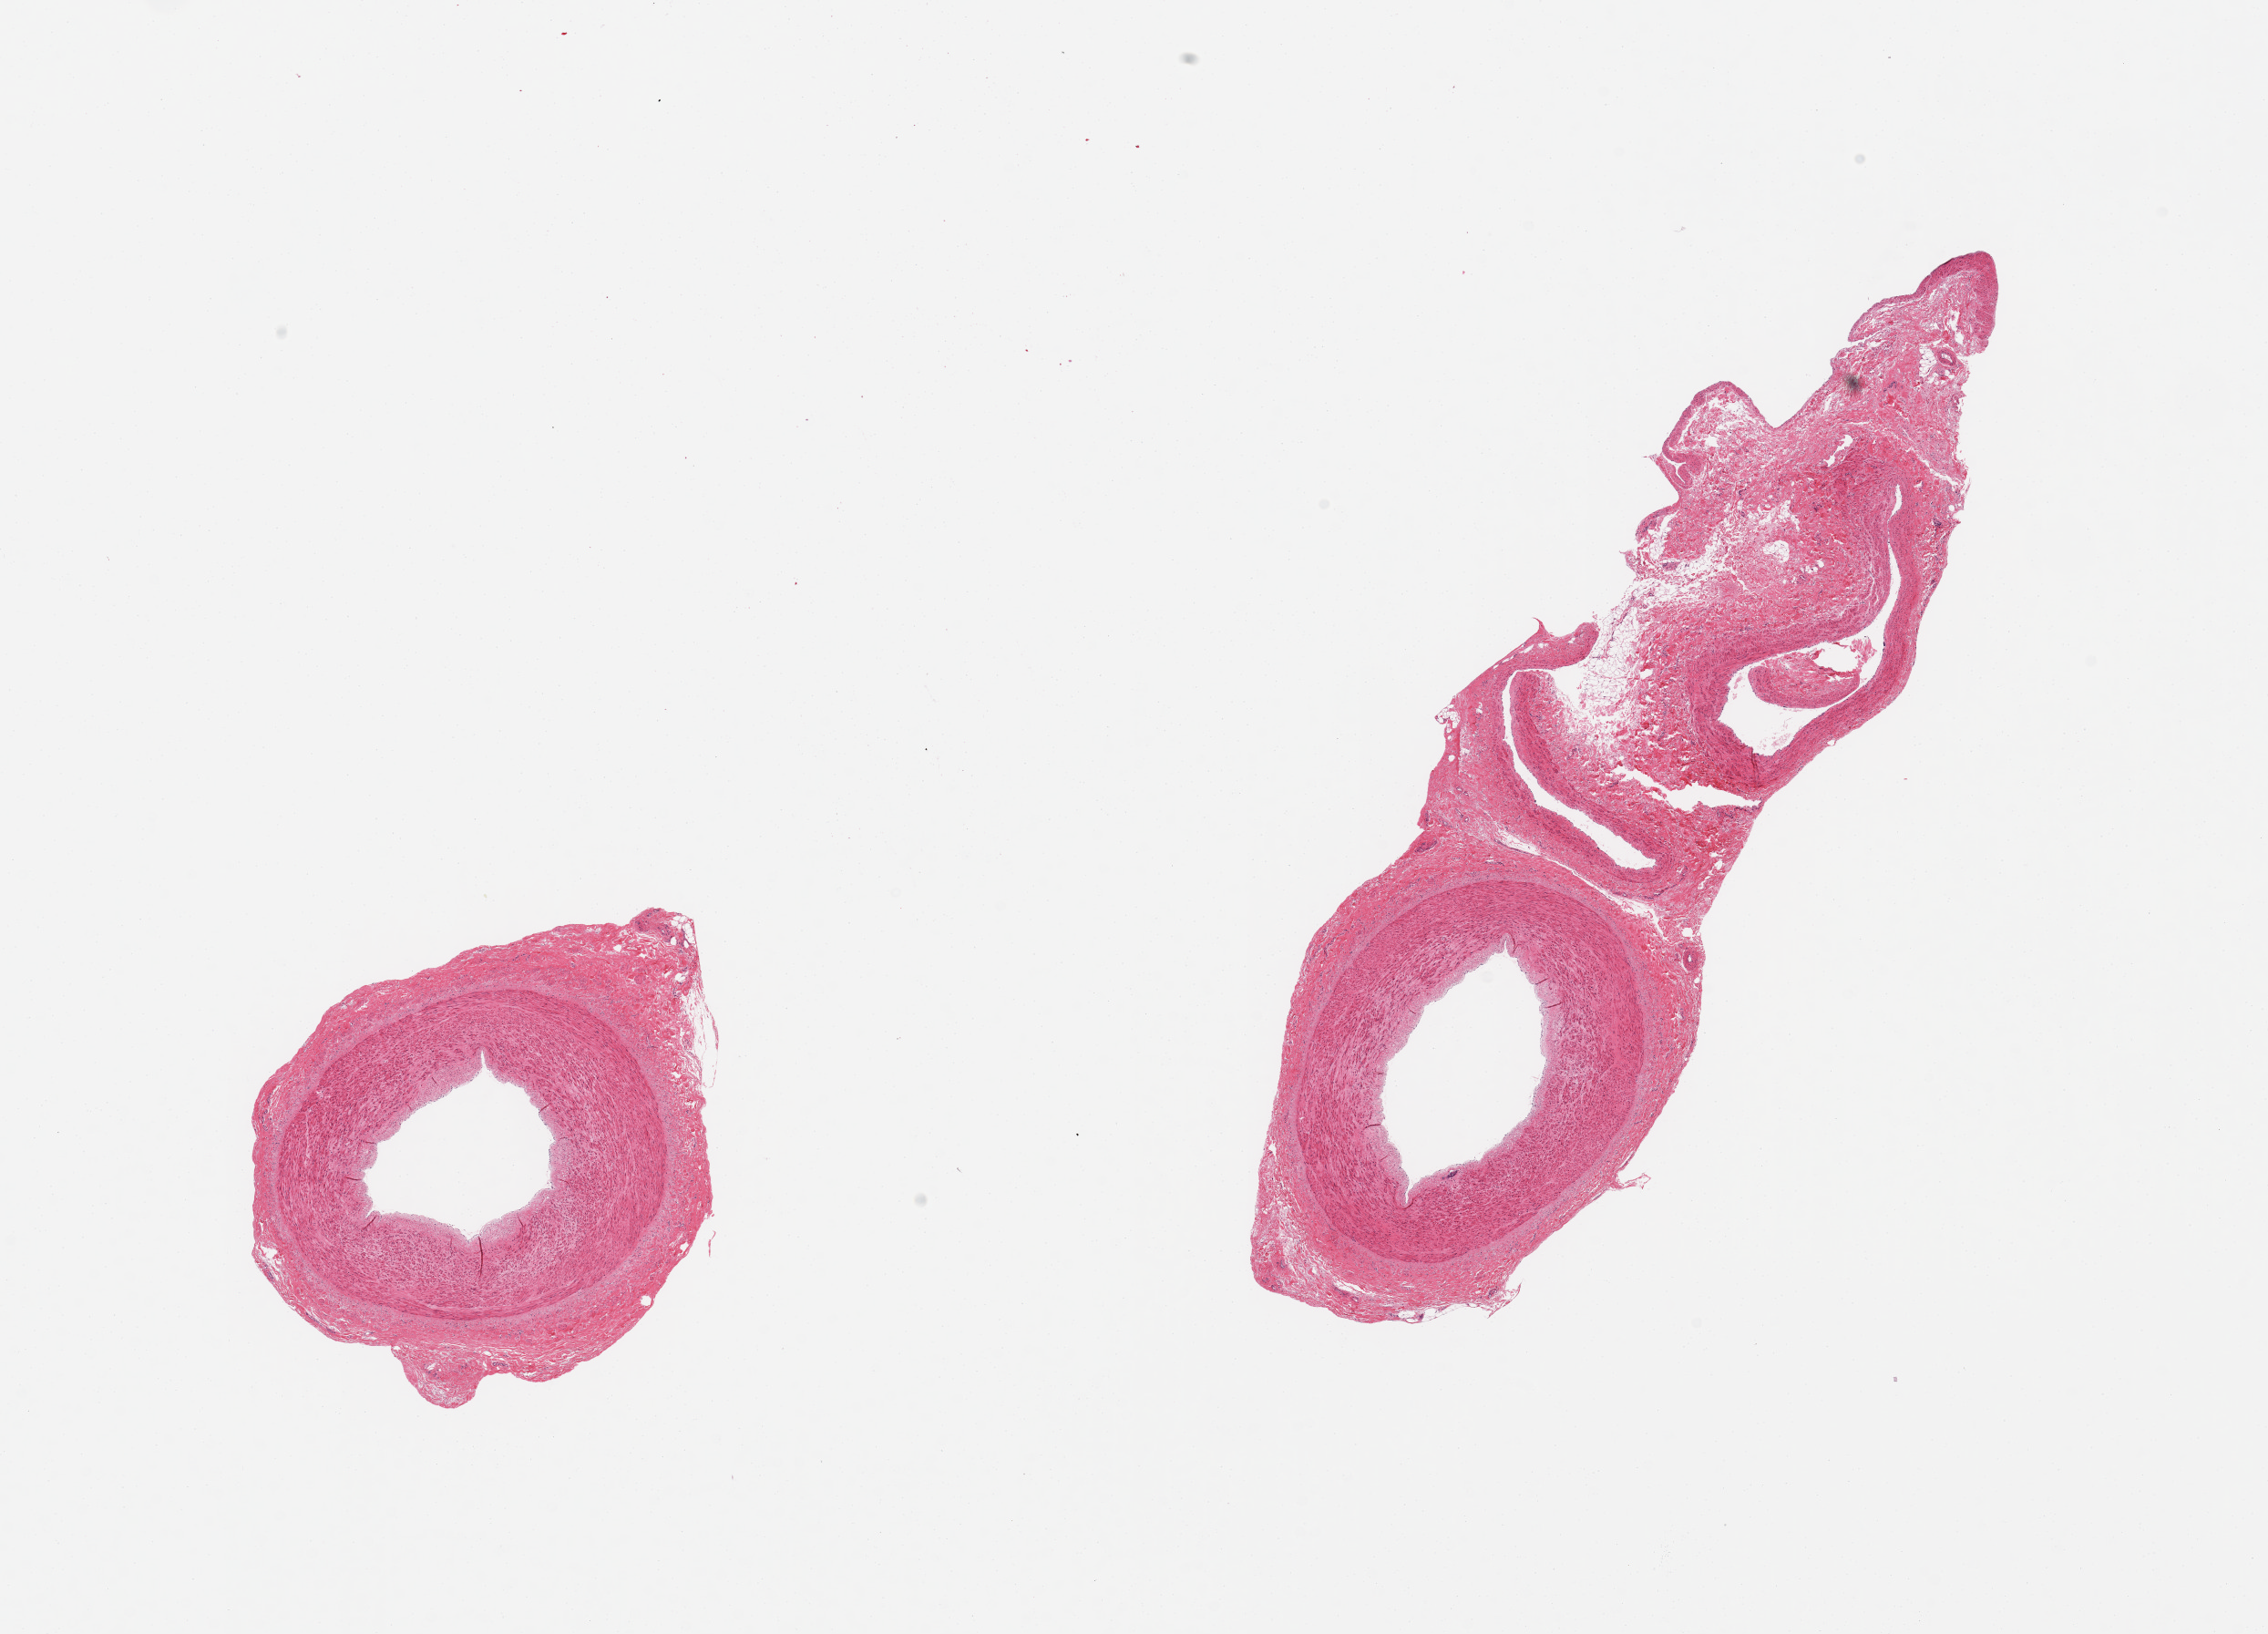
Whole-slide image, hematoxylin and eosin (H&E) stain, a low-resolution overview of the entire scanned area, about 19.7 x 14.2 mm (from a 20x scan). PAXgene-fixed paraffin-embedded (PFPE) section. Target tissue: tibial artery. Donor tissue sample. Female donor.
- review note (as recorded): 2 pieces; essentially free of plaque